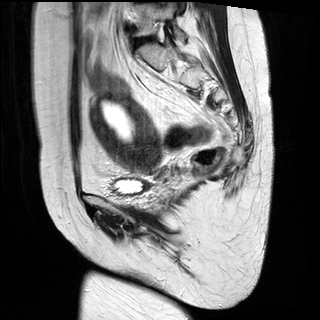
Pelvic MRI for cervical cancer, one sagittal slice. Position 10 of 28 along the scan axis. T2-weighted. 1.5 T. TE 89 ms, TR 2740 ms. 320 × 320 image matrix. Female patient, age 49 years.
Annotated regions visible in this slice (manually delineated by an expert):
- uterus and cervix: bounding box [x1, y1, x2, y2] px = [87, 89, 162, 174]